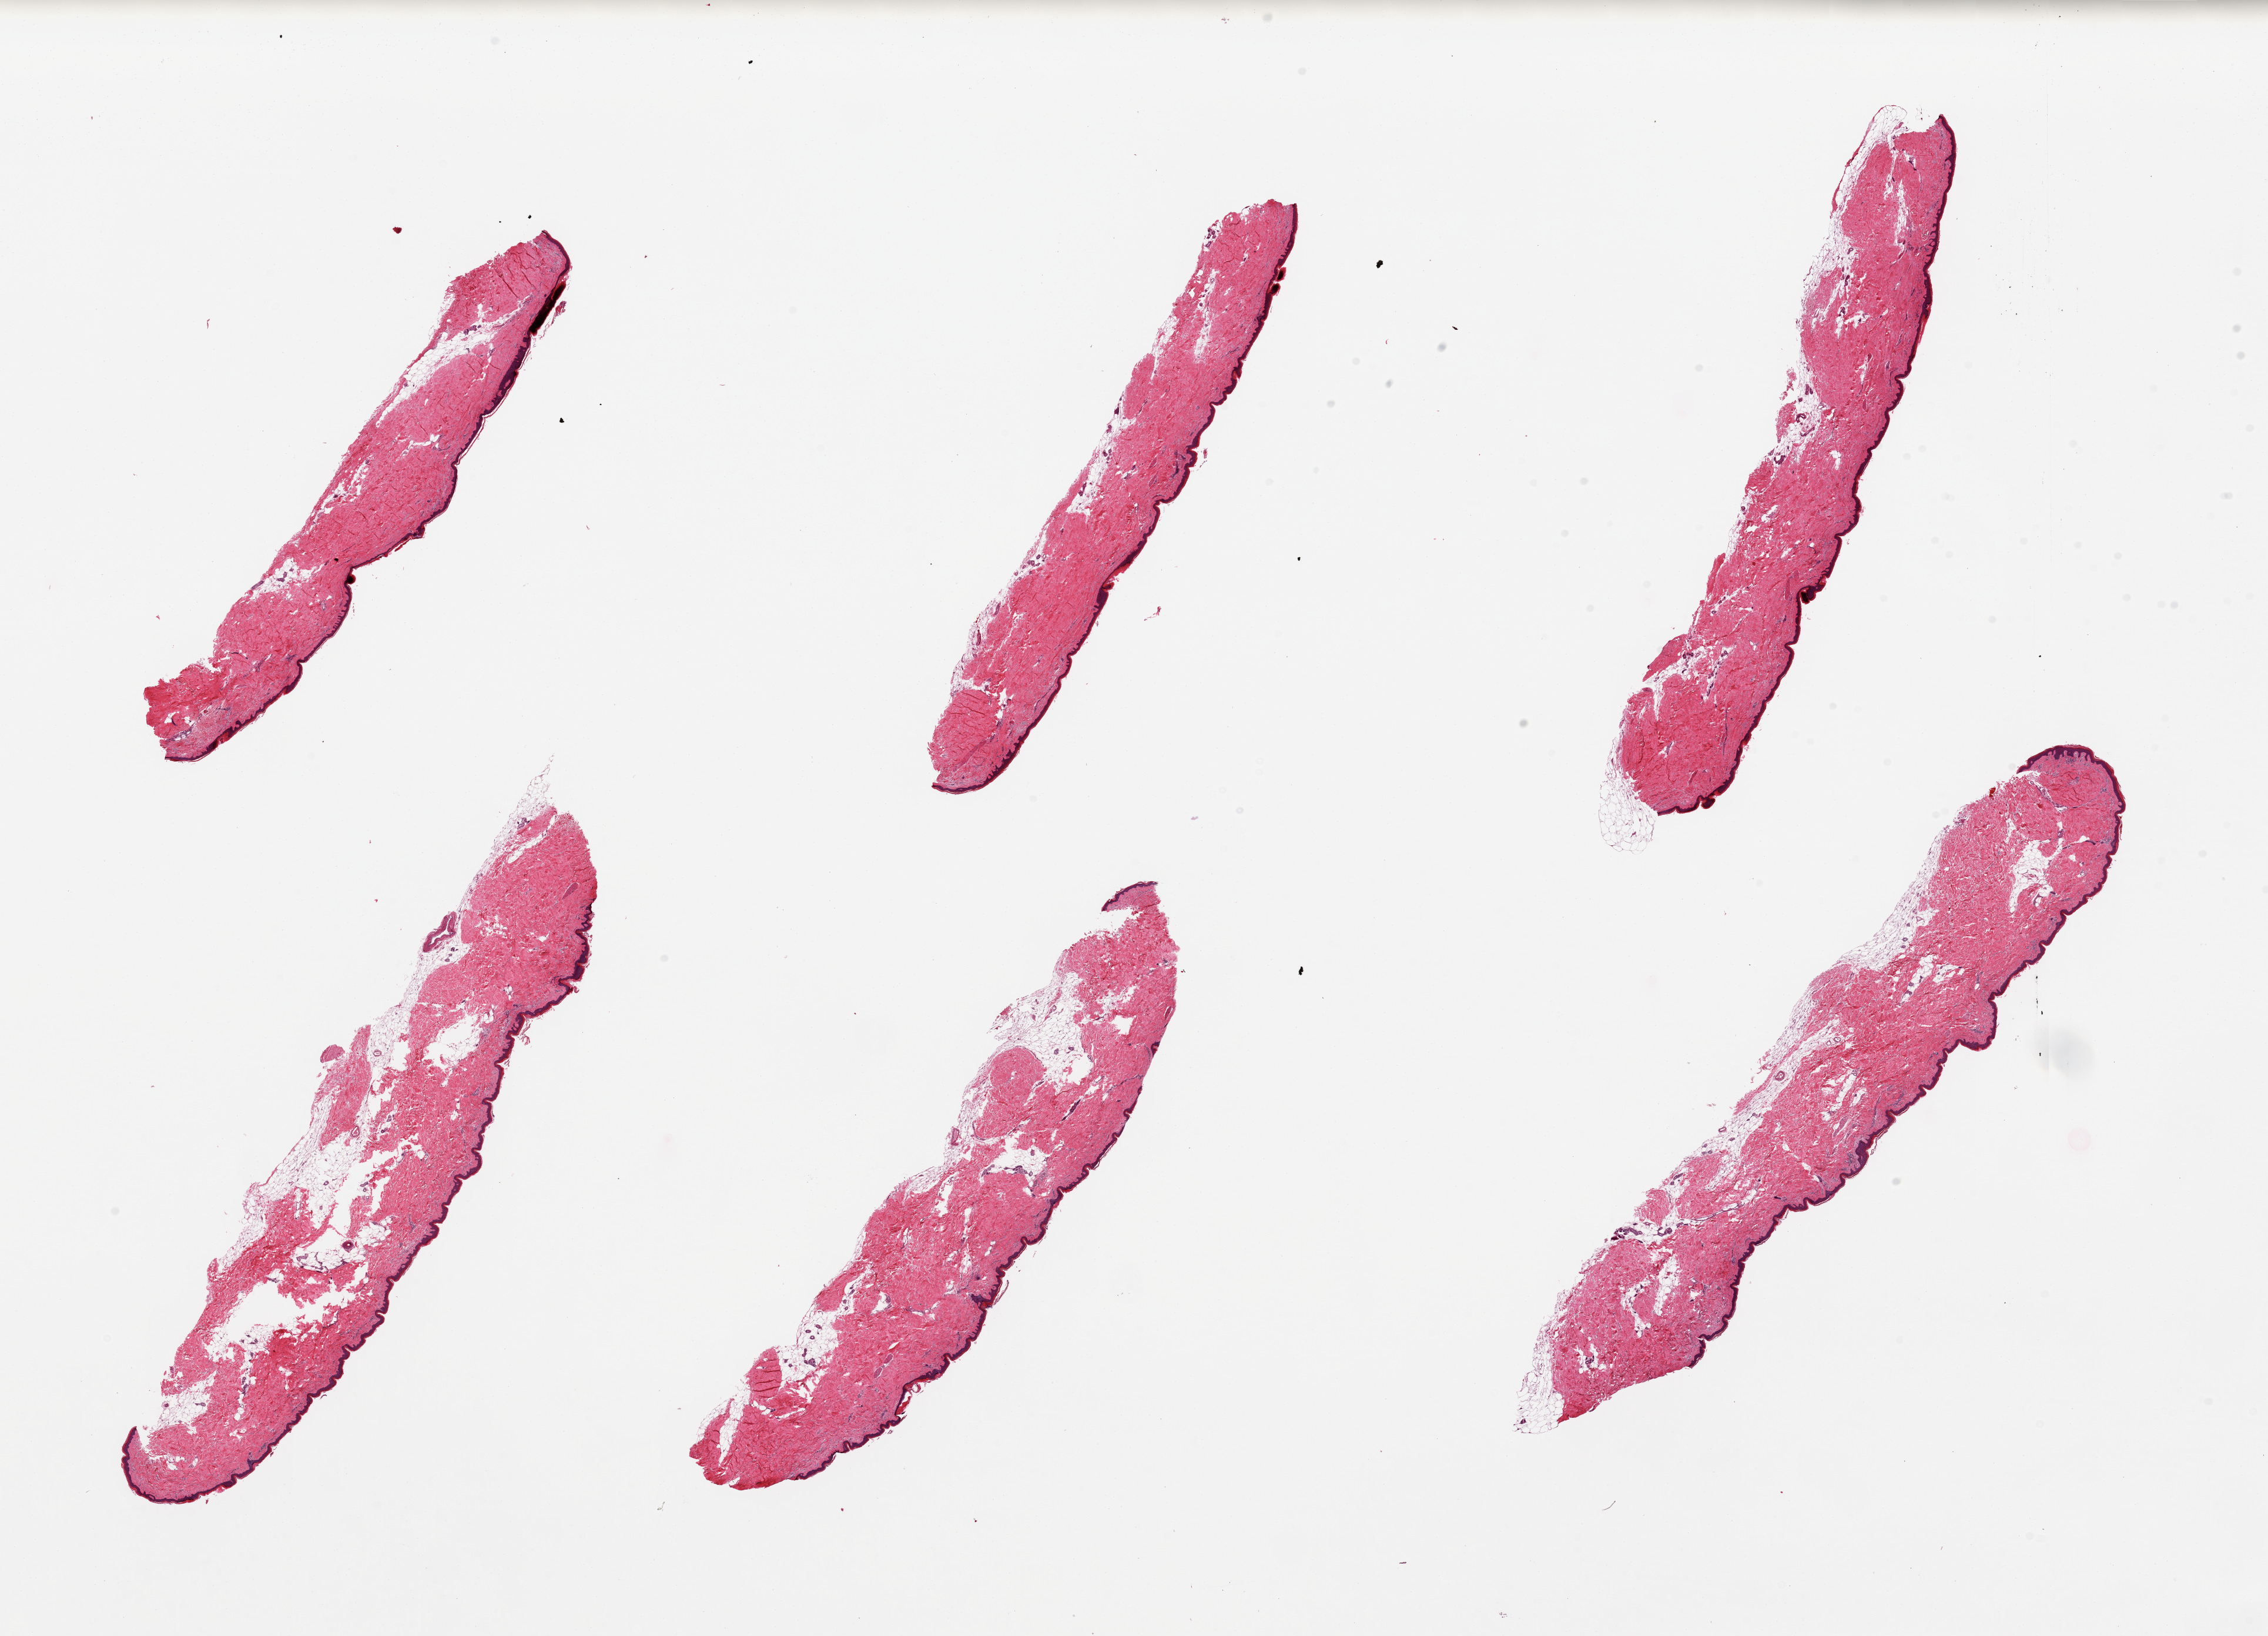
Digitized hematoxylin and eosin (H&E)-stained section, brightfield, whole scanned area (about 30.5 x 22.0 mm, acquisition: 20x scan) shown as a low-resolution overview, PAXgene-fixed, paraffin-embedded tissue, target tissue: skin of lower leg, tissue donor sample. Donor sex: female.
* pathologist's review note for this sample: 6 pieces, up to 12x2.5mm; squamous epithelium is ~1-2% thickness